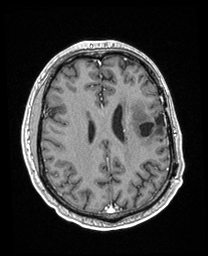
Brain MRI from a brain-tumour surgery series, one axial slice; T1-weighted post-contrast; 208 × 256 image matrix, field of view 211 × 260 mm. From the clinical record (not read from this slice): histopathology: Astrocytoma; WHO grade: 3; IDH mutation: yes; tumour location: Left Insular.
Structures marked on this image (manually delineated by an expert):
- previous resection cavity: bounding box <140,114,165,137> (left, top, right, bottom; pixels)